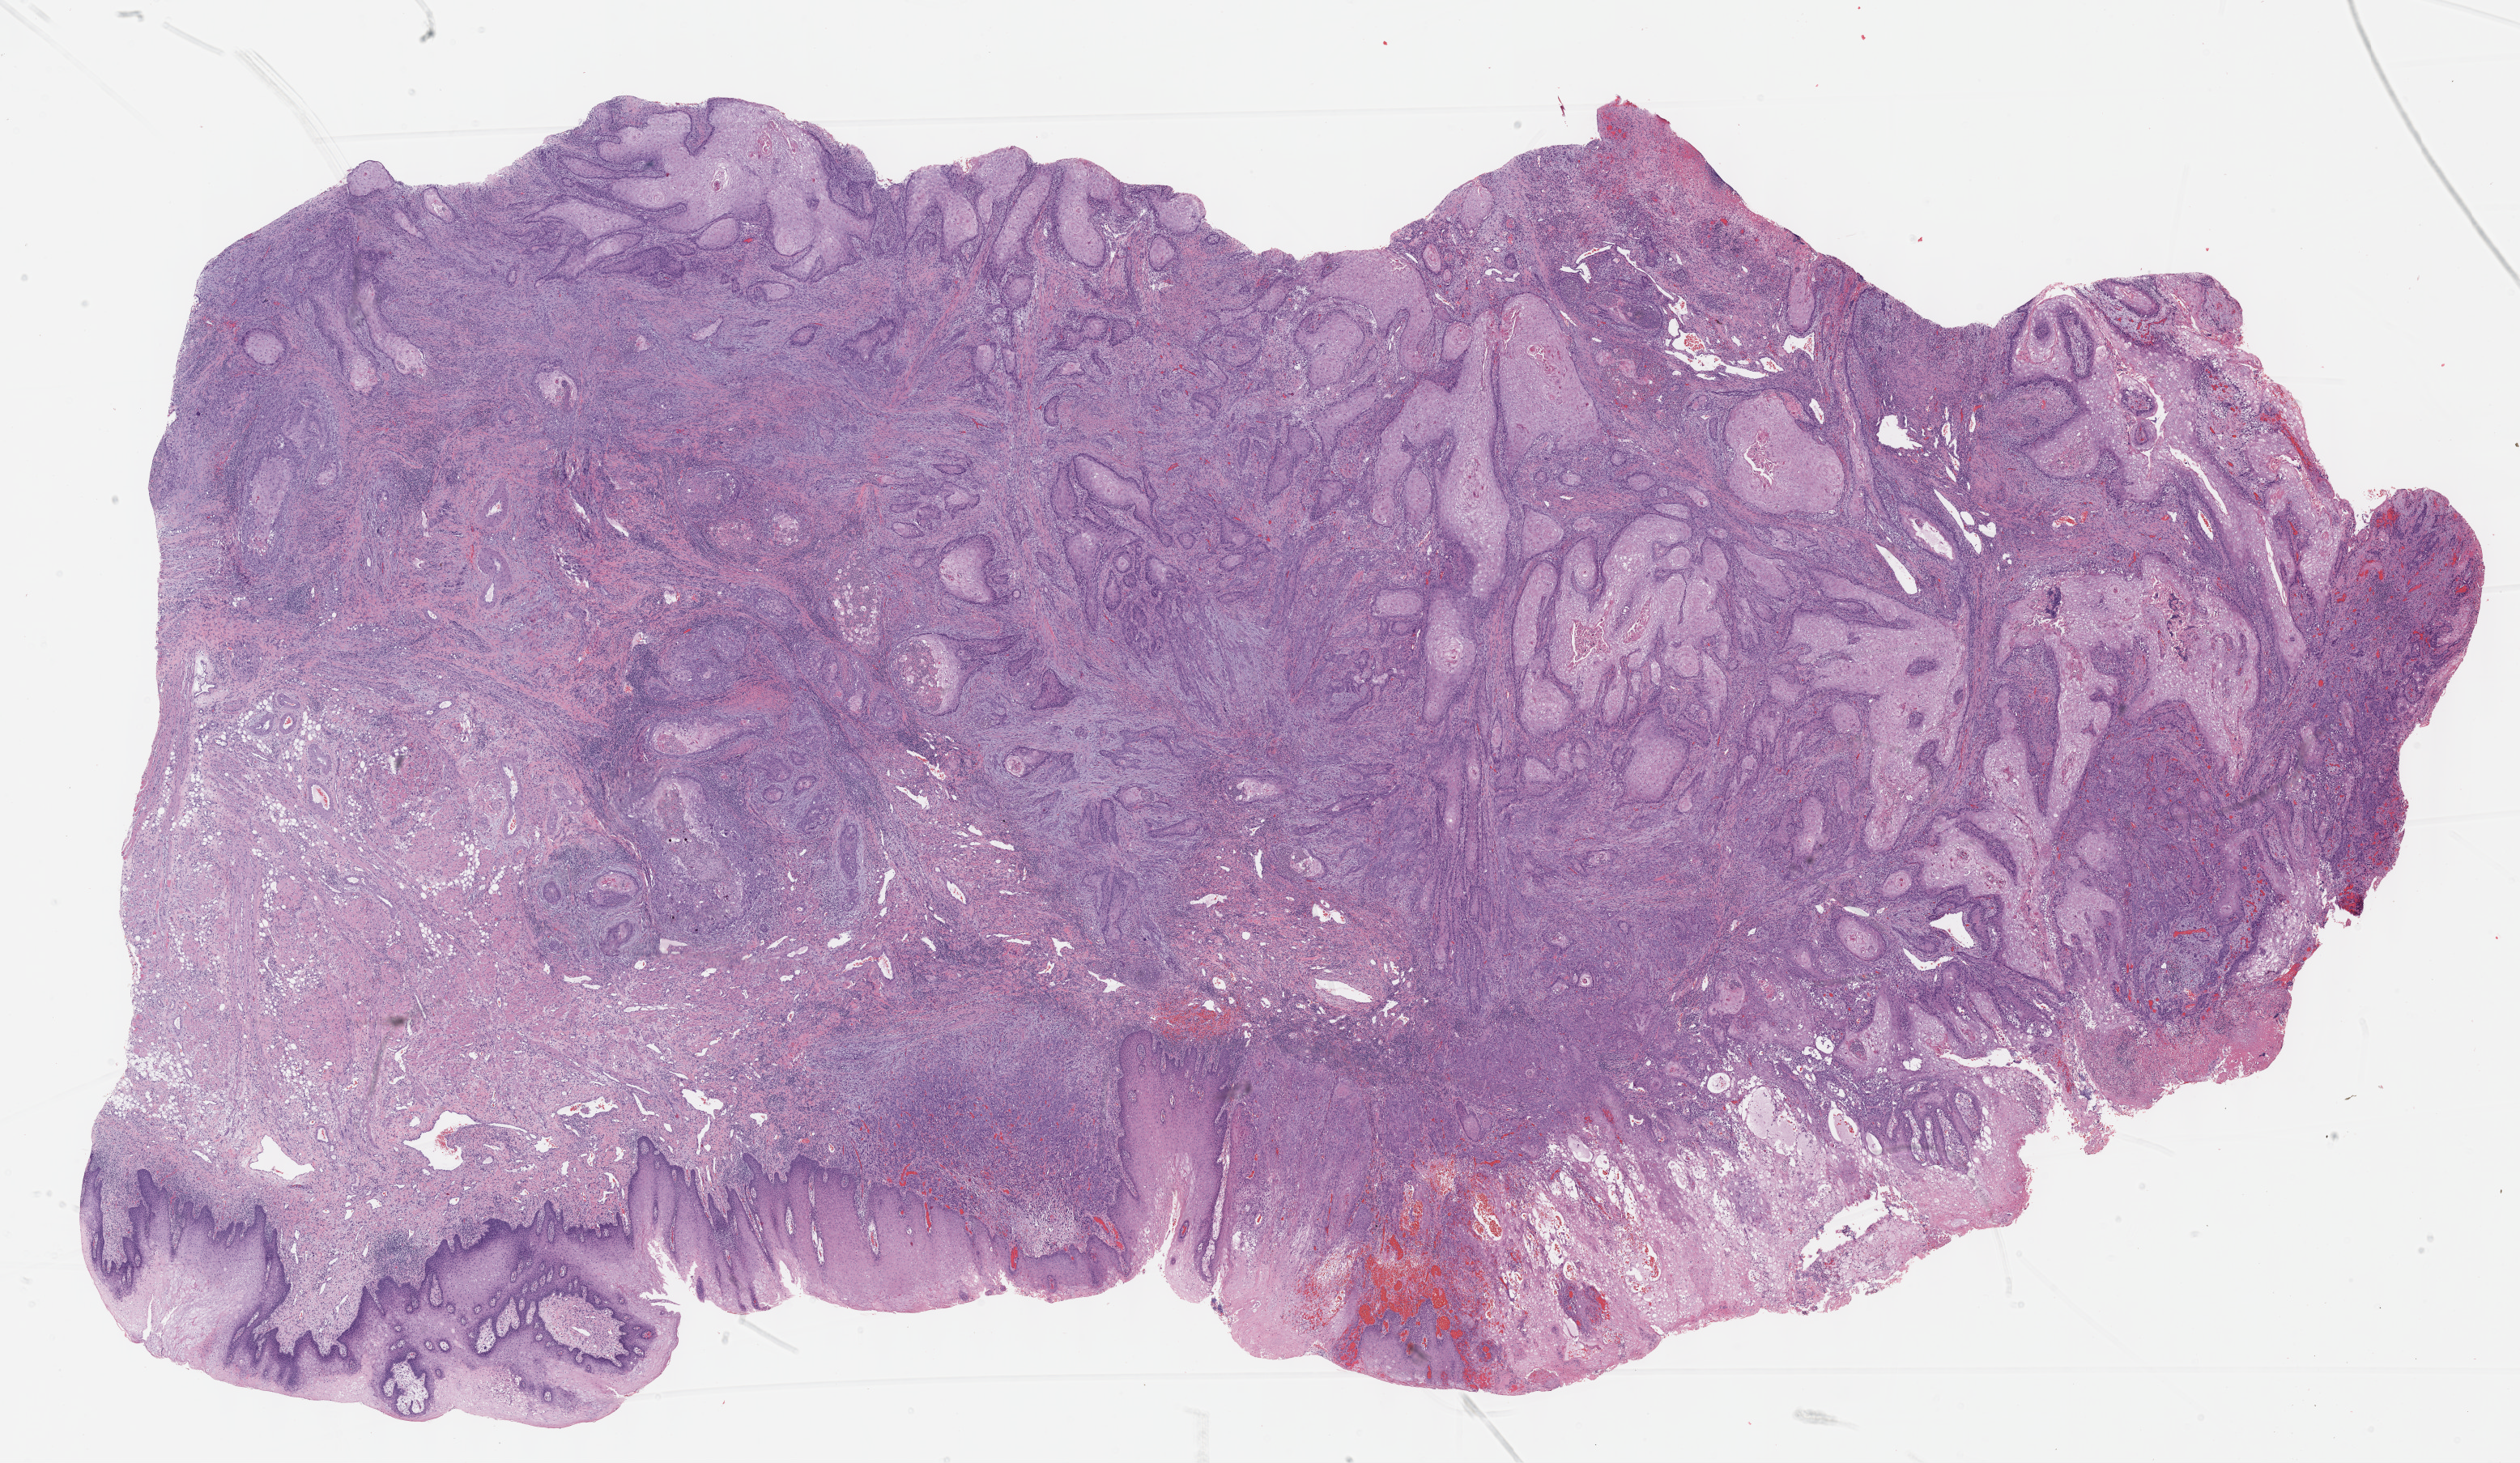
Digitized H&E tissue section (whole slide), shown as a low-resolution overview of the whole scanned area (about 25.1 x 14.6 mm, slide scanned at 40x). FFPE section. Head and neck, primary tumour sample. Male, age 69 years at initial diagnosis. Histologic grade: G2 (moderately differentiated).
AJCC pathologic stage: IVA (7th edition). Diagnosis: Squamous cell carcinoma, NOS (tongue, NOS).